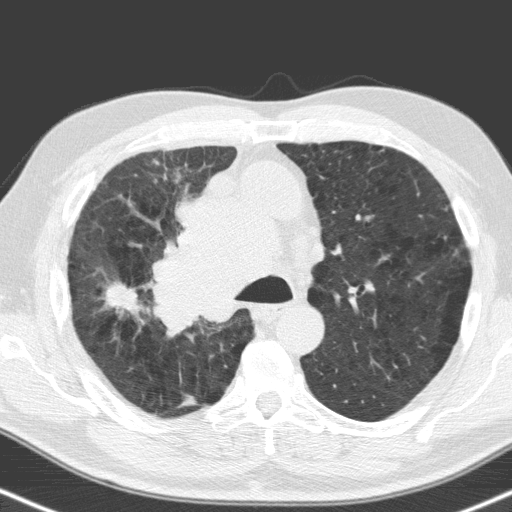
Low-dose screening chest CT, one axial slice; position 112 of 160 along the scan axis; 120 kVp; lung window (W 1500 / L -600 HU); 512 × 512 image matrix, field of view 324 × 324 mm.
Outlined on this slice (outlined manually by an expert reader):
- lesion 1 (tumor, hilum of right lung): bounding box [x1, y1, x2, y2] px = [155, 173, 262, 329]
- lesion 2 (tumor, upper lobe of right lung): [107, 284, 141, 309]